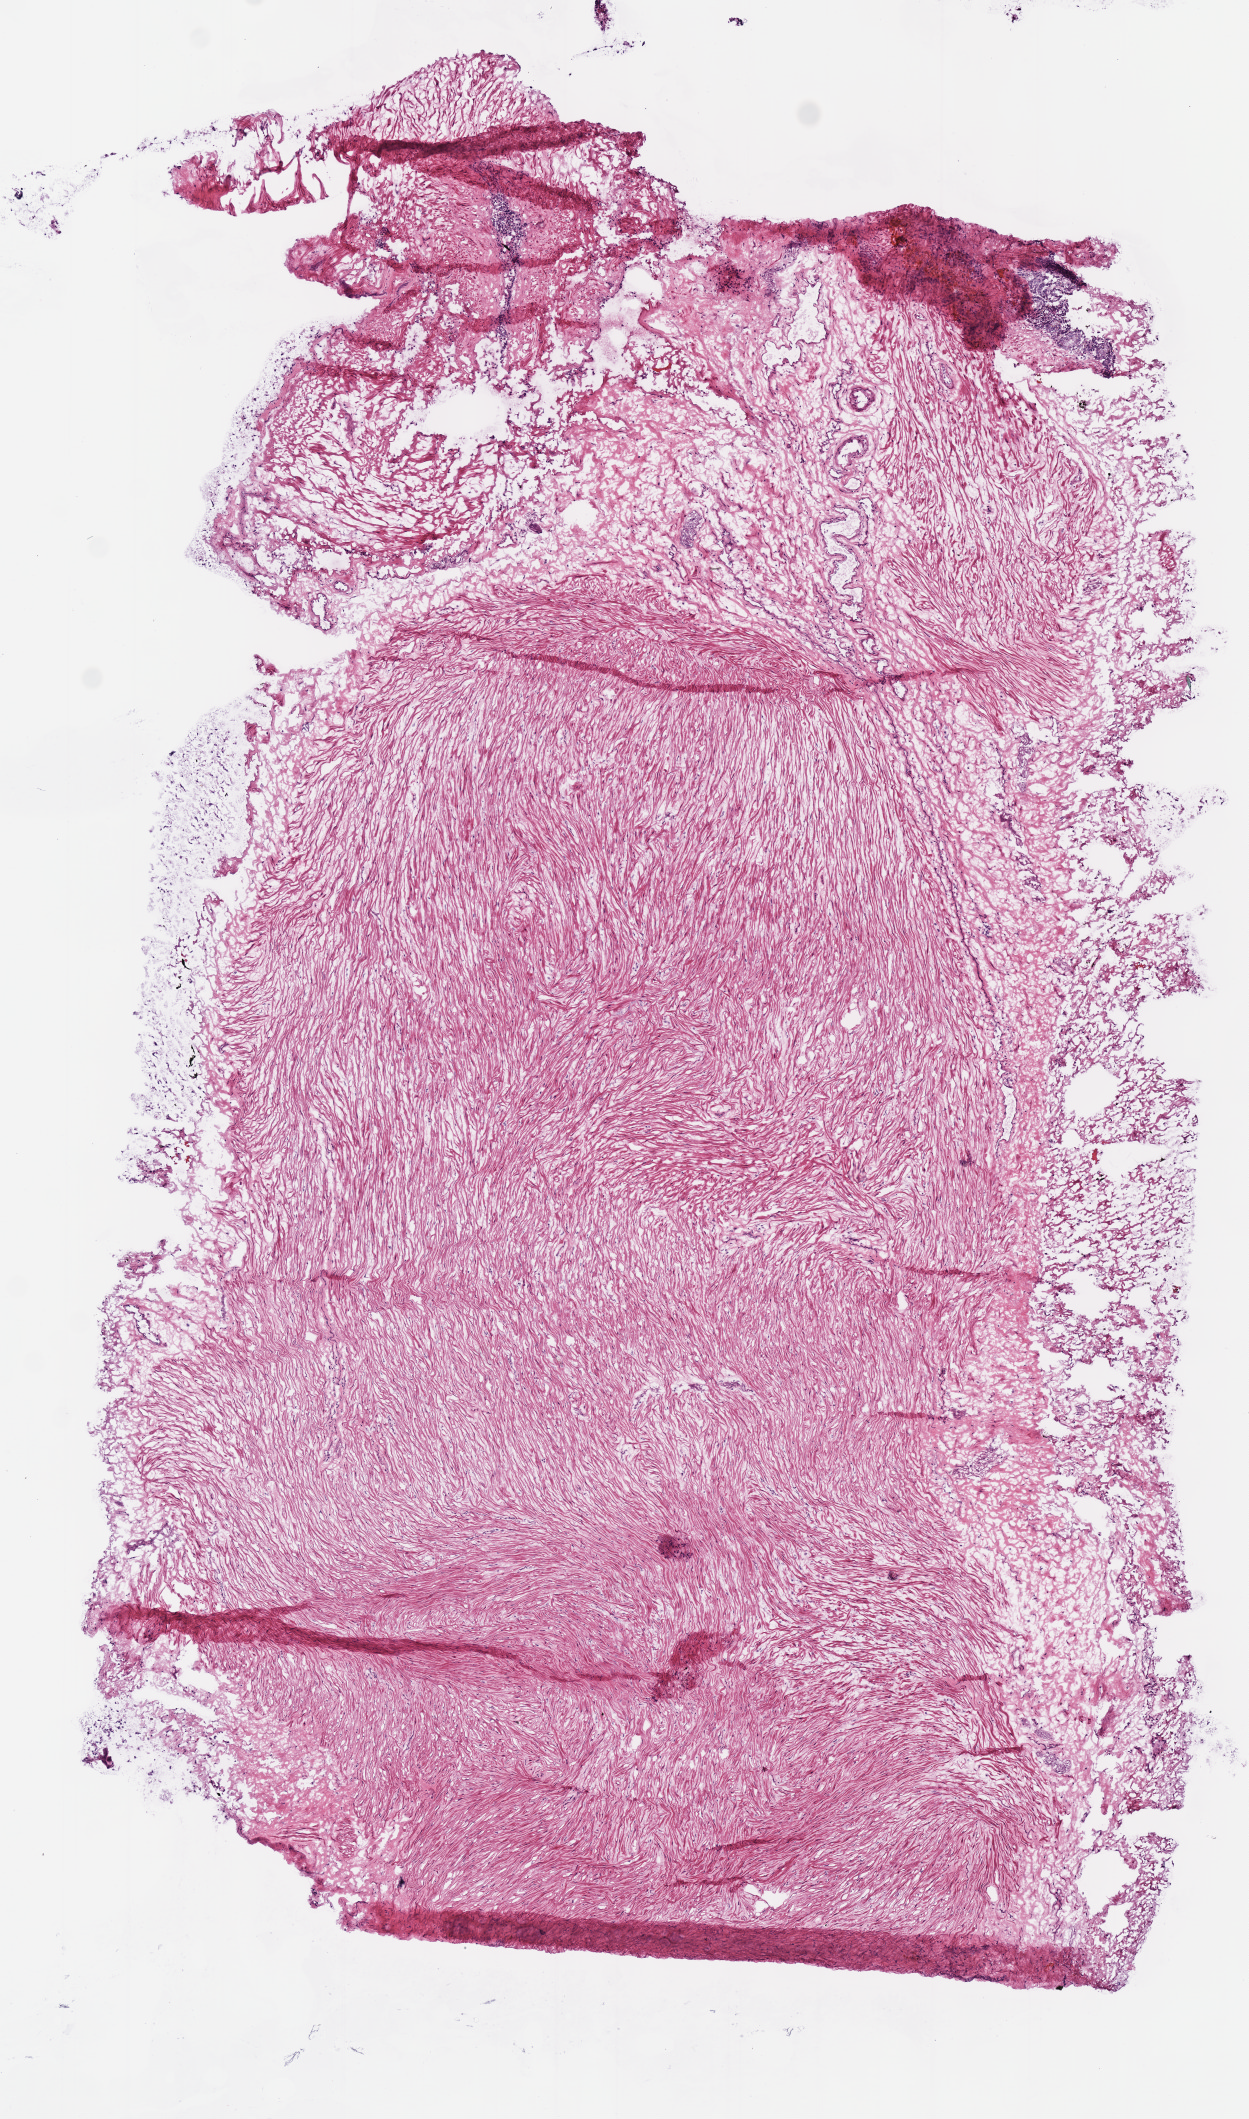
Whole-slide histology image, H&E, whole scanned area (about 4.9 x 8.4 mm, slide scanned at 40x) shown as a low-resolution overview; frozen section from the top of the tissue portion; solid tissue normal (non-tumour tissue) sample from the prostate. Male patient; age at initial diagnosis 65 years.
This section: solid tissue normal sample (biorepository sample class). Patient diagnosis: Acinar cell carcinoma (prostate gland).